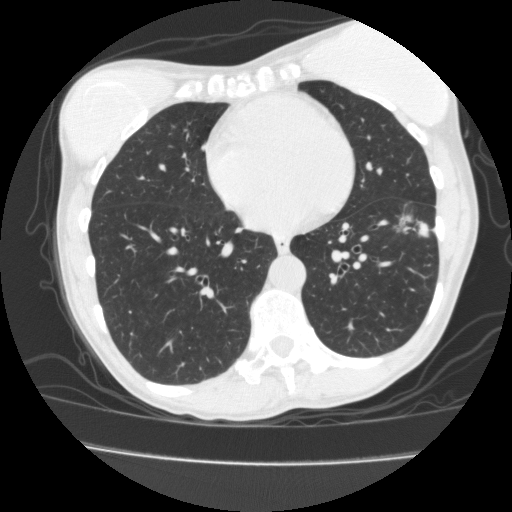
Low-dose screening chest CT, one axial slice; slice 66 of 171 in the series (ordered by position); reconstruction kernel FC10; 120 kVp; lung window (W 1500 / L -600 HU); 2 mm slice thickness; 512 × 512 image matrix, field of view 339 × 339 mm.
Annotated regions visible in this slice (manually delineated by an expert):
- lesion 1 (tumor, lower lobe of left lung): box from (x=419, y=222) to (x=428, y=235) px